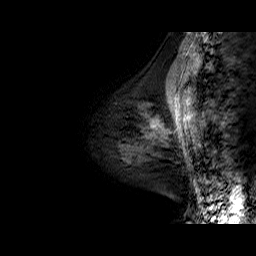
Breast MRI (dynamic contrast-enhanced), one sagittal slice; position 17 of 60 along the scan axis; dynamic contrast-enhanced series, time point 2 of 6 at this slice position (early post-contrast); 1.5 T; TE 6.4 ms, TR 32.9 ms; 4 mm slice thickness; 256 × 256 image matrix, field of view 200 × 200 mm. Female patient. From the clinical record (not read from this slice): setting: breast cancer imaged before/during neoadjuvant chemotherapy; receptor status: HR-positive, HER2-negative.
Outlined on this slice (semi-automatically segmented with operator editing):
- analysis volume of interest (the breast-tissue region the enhancement analysis was run in; not a lesion): bounding box (x1, y1, x2, y2) in pixels: (106, 86, 164, 171)
- tumour enhancement mask (voxels above the 100 % enhancement threshold inside the analysis volume of interest): (153, 126, 156, 128)